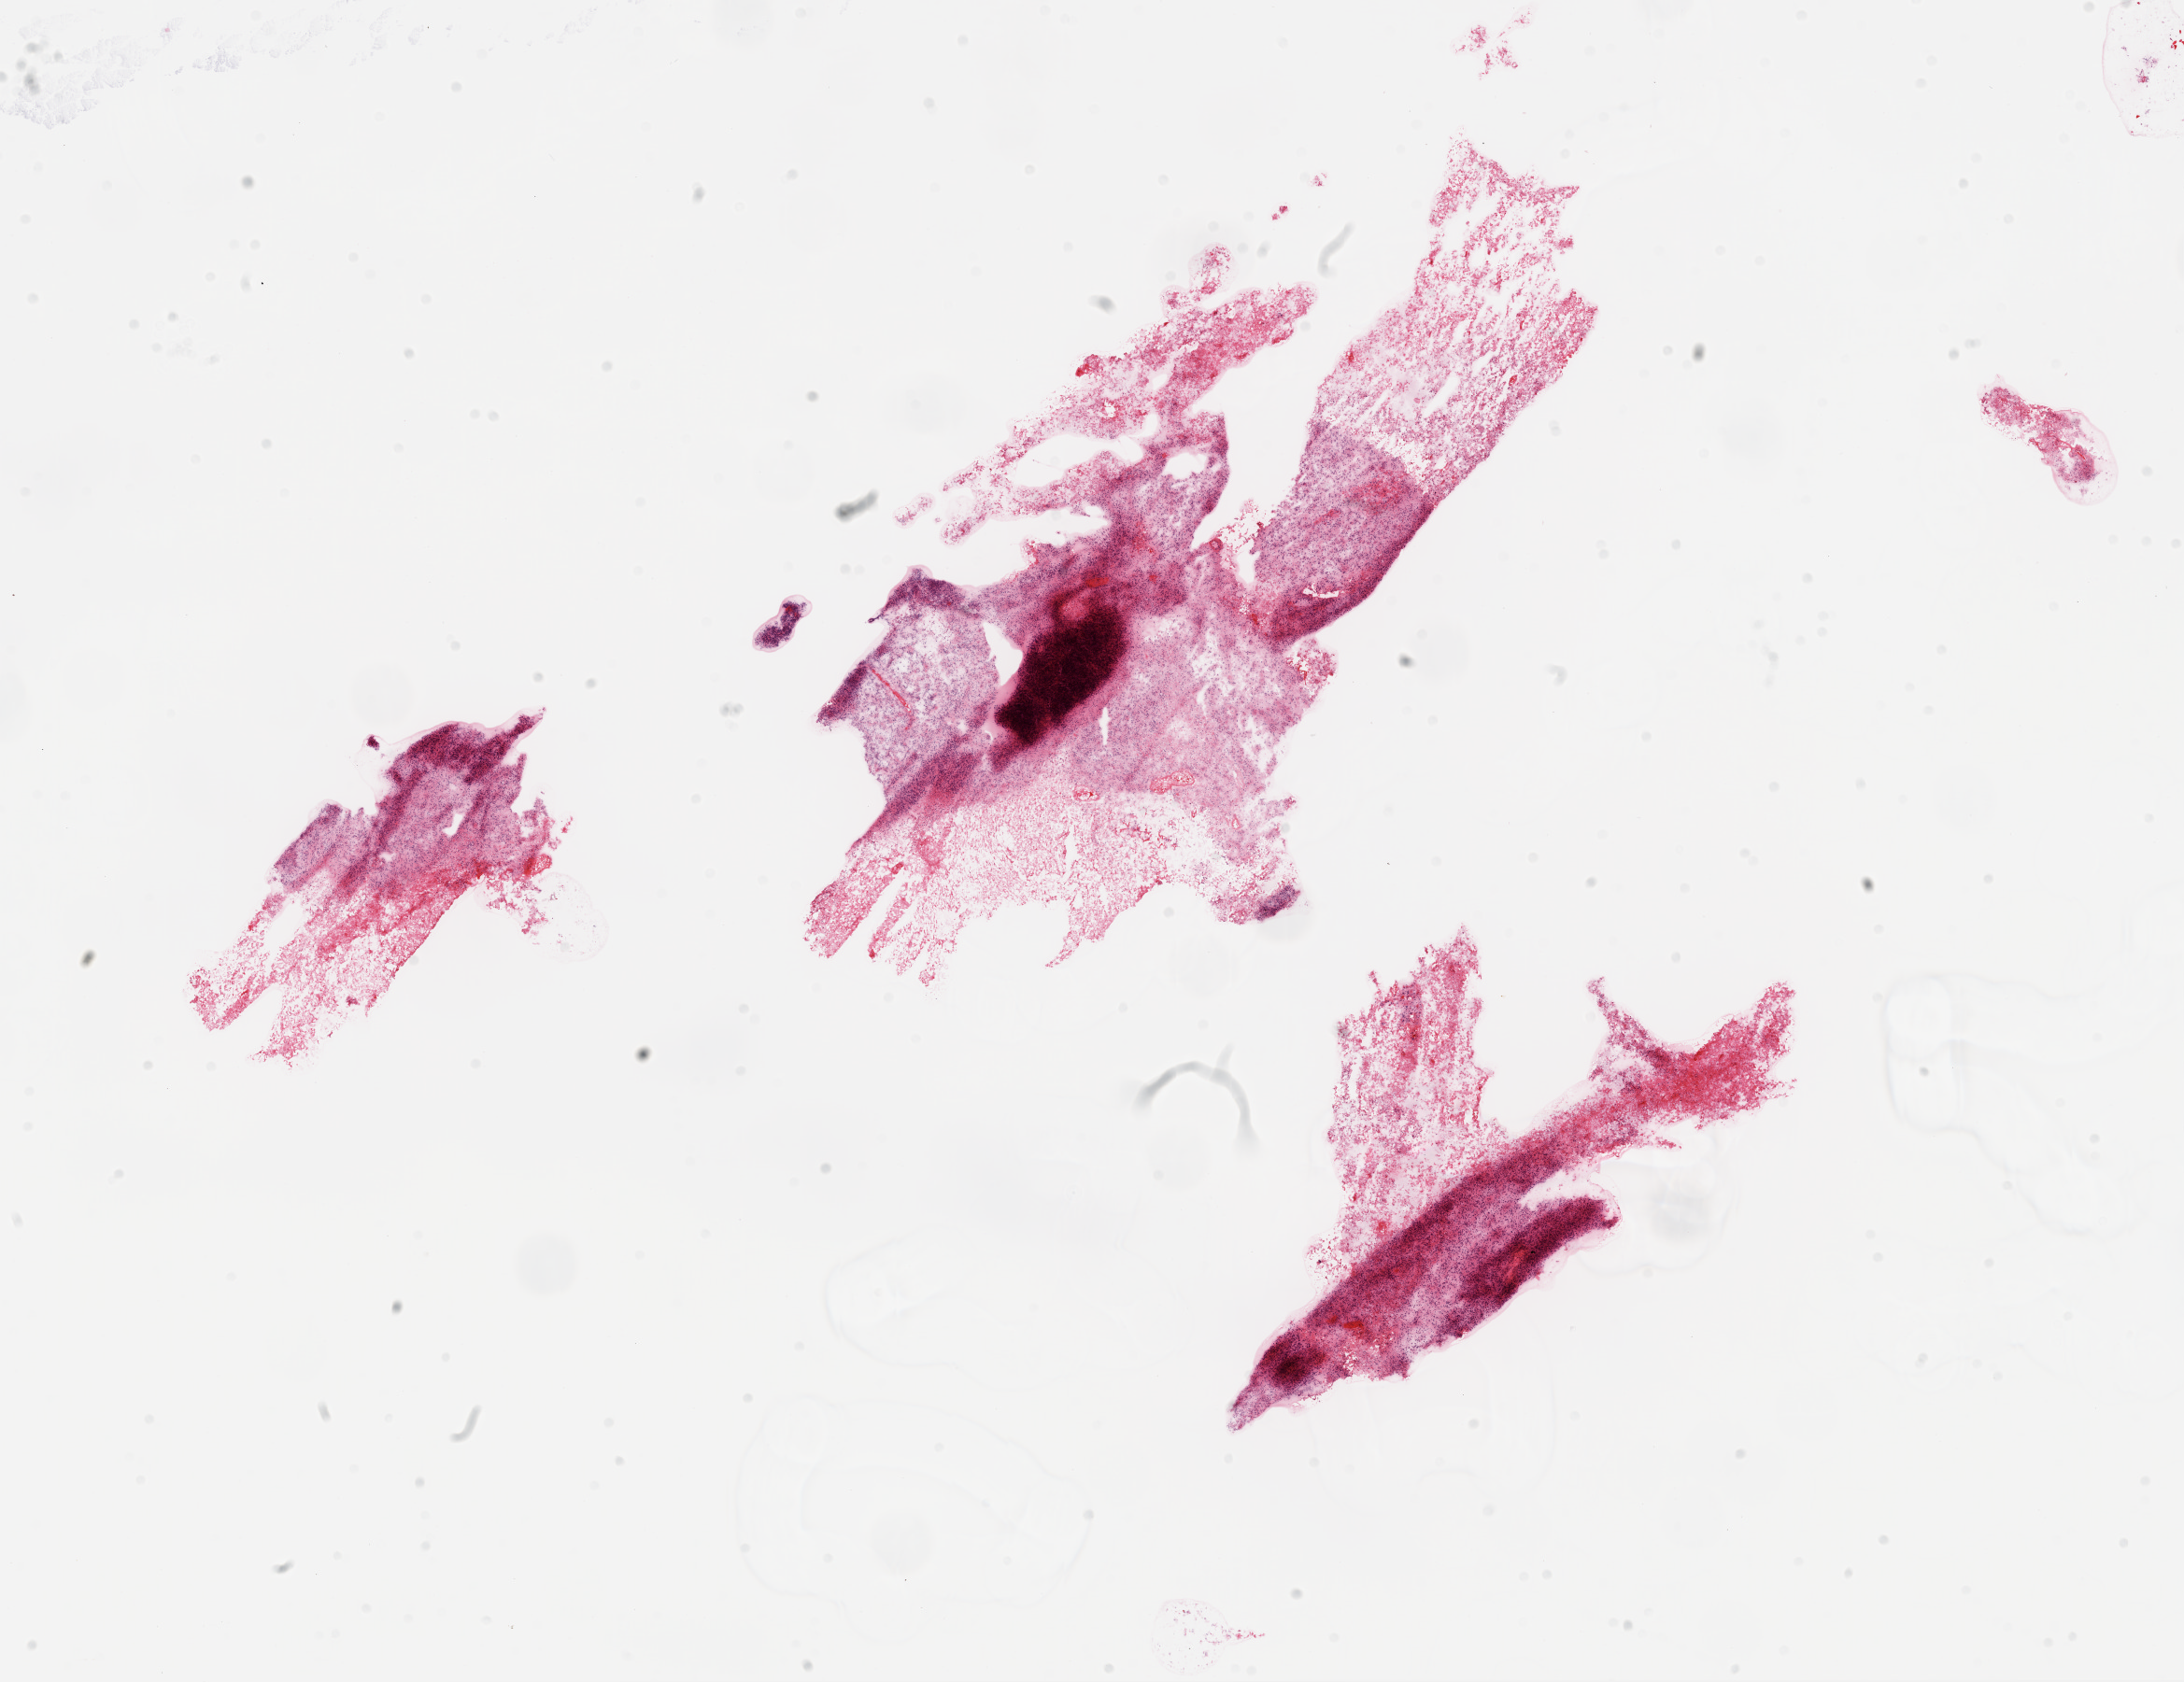
Whole-slide histology image, H&E-stained — low-resolution overview of the scanned area, about 18.9 x 14.5 mm, frozen section from the bottom of the tissue portion, brain, primary tumour sample. Patient: male, age at initial diagnosis 63 years. Composition of this section per pathologist review: tumour cells 70%, tumour nuclei 95%, normal cells 0%, stromal cells 0%, necrosis 30%.
Diagnosis: Glioblastoma.